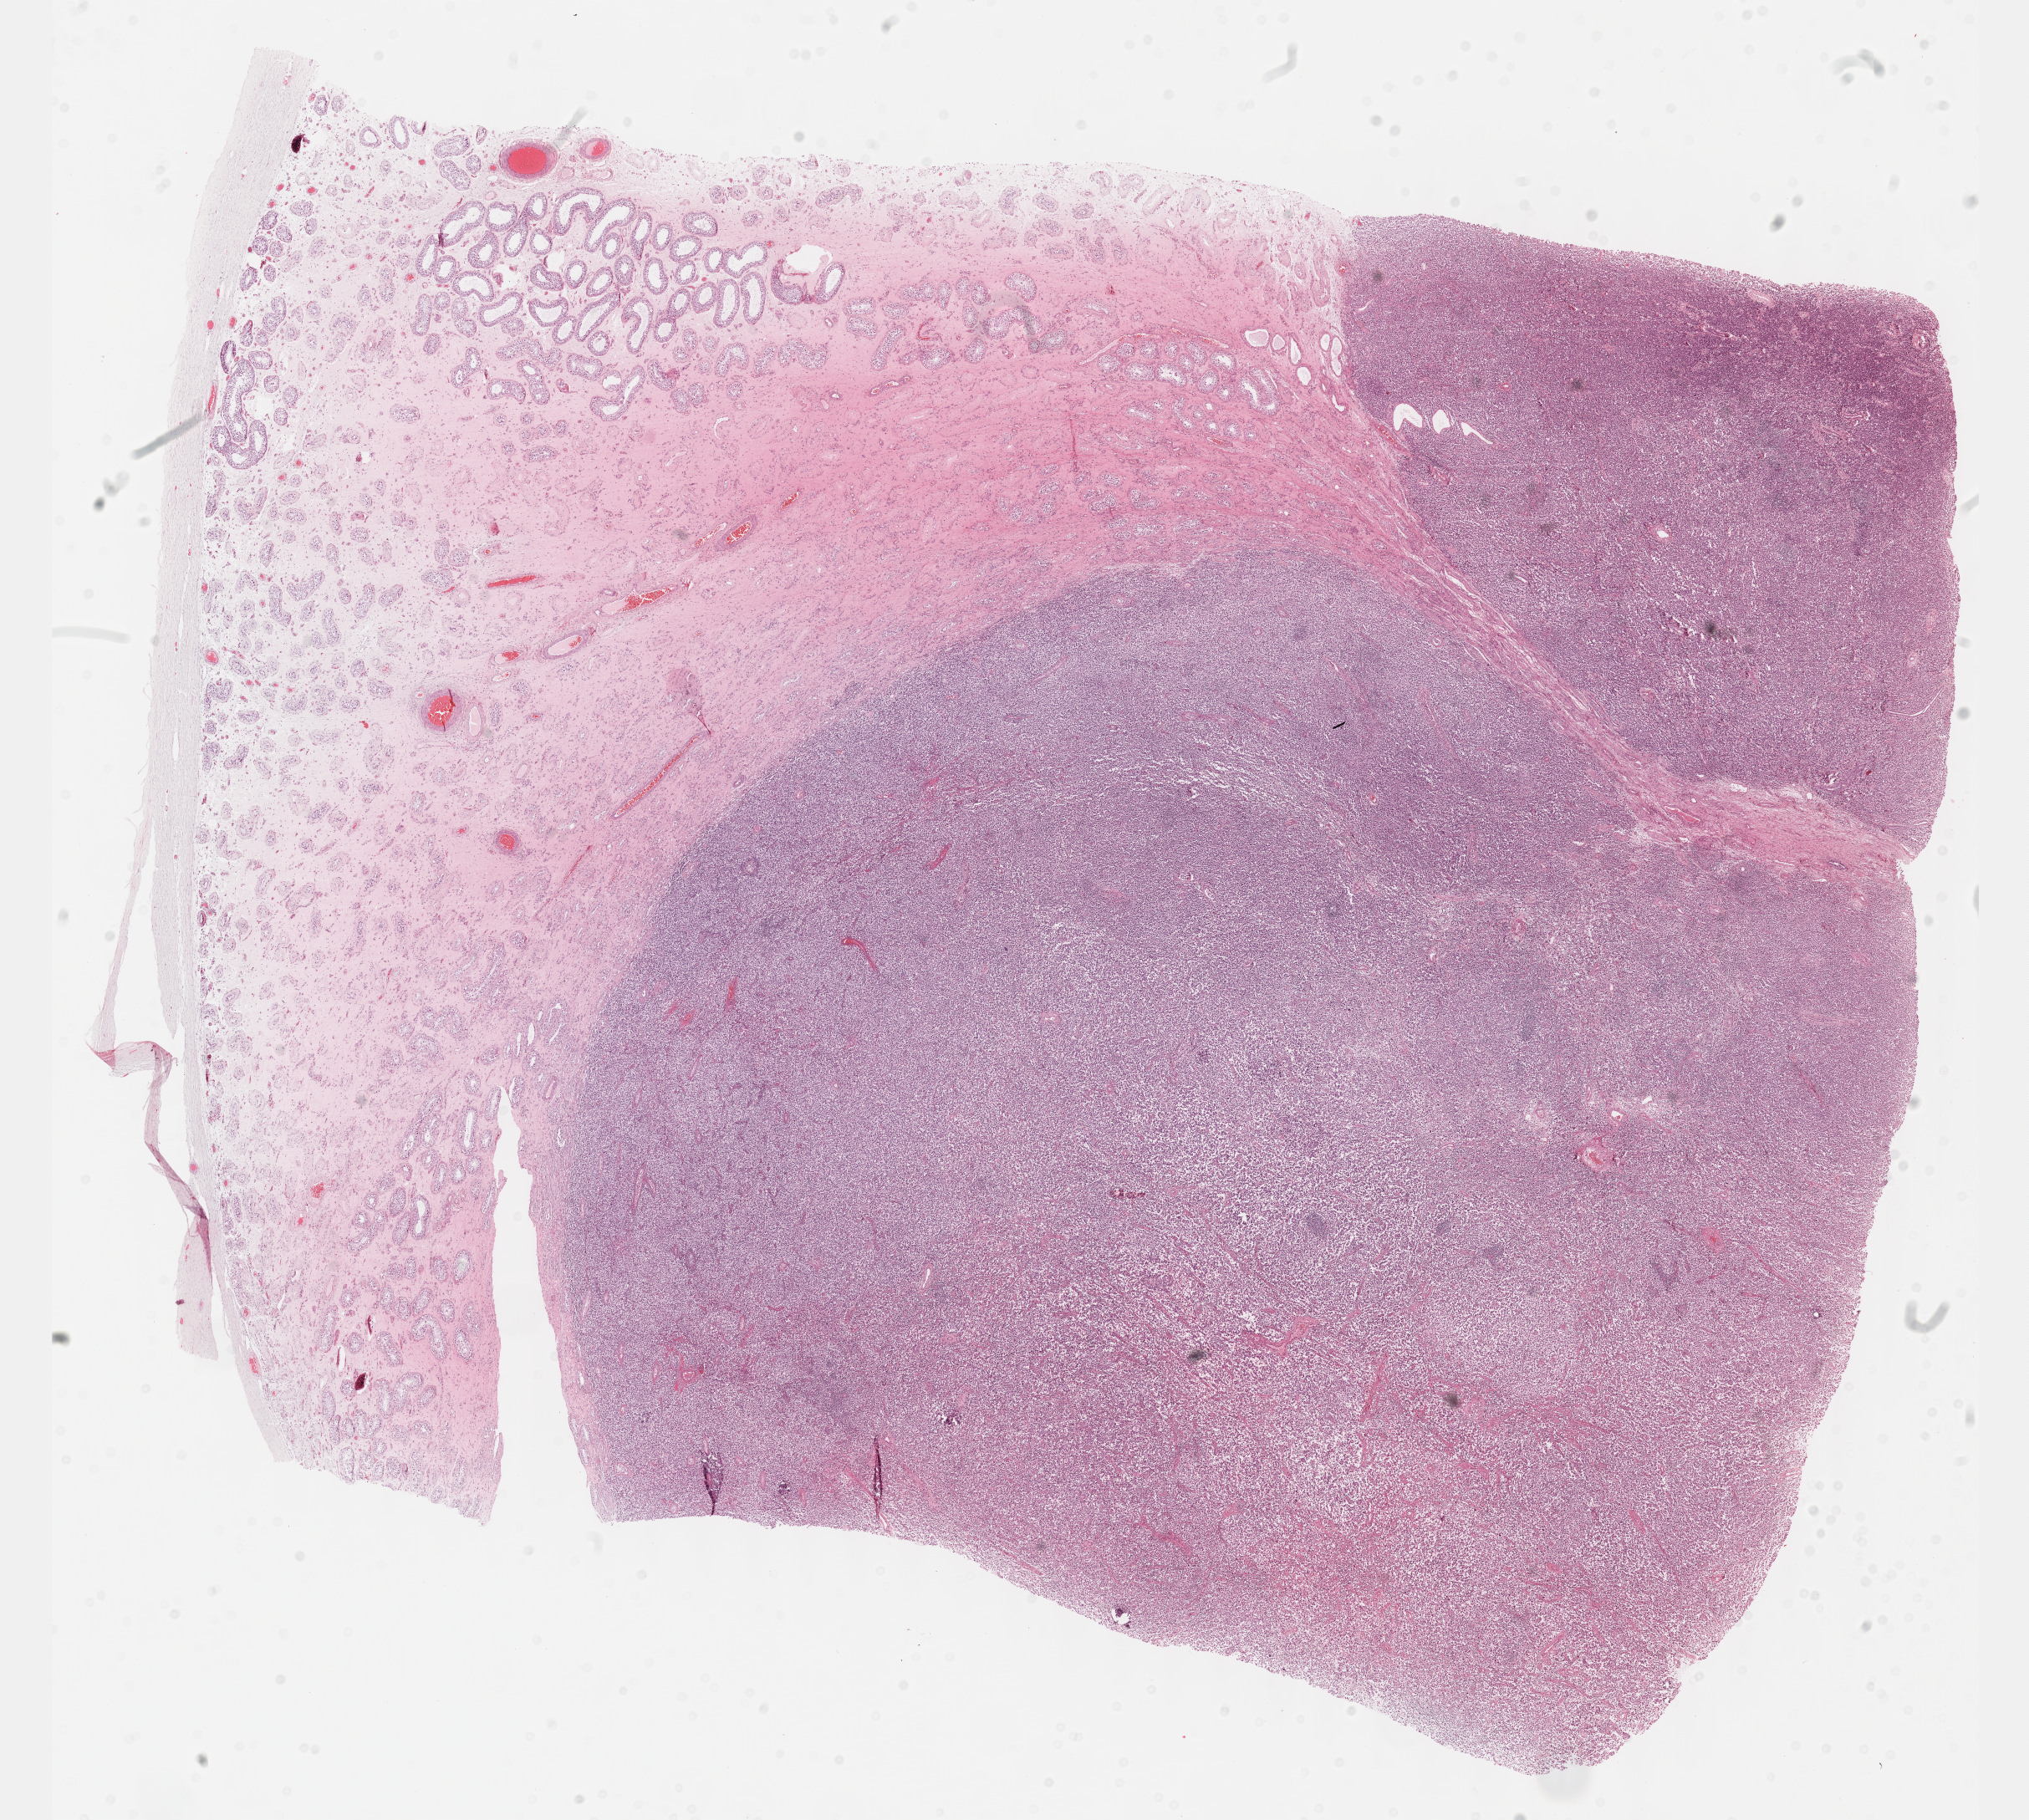
H&E-stained whole-slide image, whole scanned area (about 19.6 x 17.6 mm, from a 40x scan) shown as a low-resolution overview, formalin-fixed paraffin-embedded (FFPE) diagnostic section, sample: primary tumour, testis. Male, age 32 years at initial diagnosis.
AJCC pathologic stage: IA (7th edition). Histologic diagnosis: Seminoma, NOS.